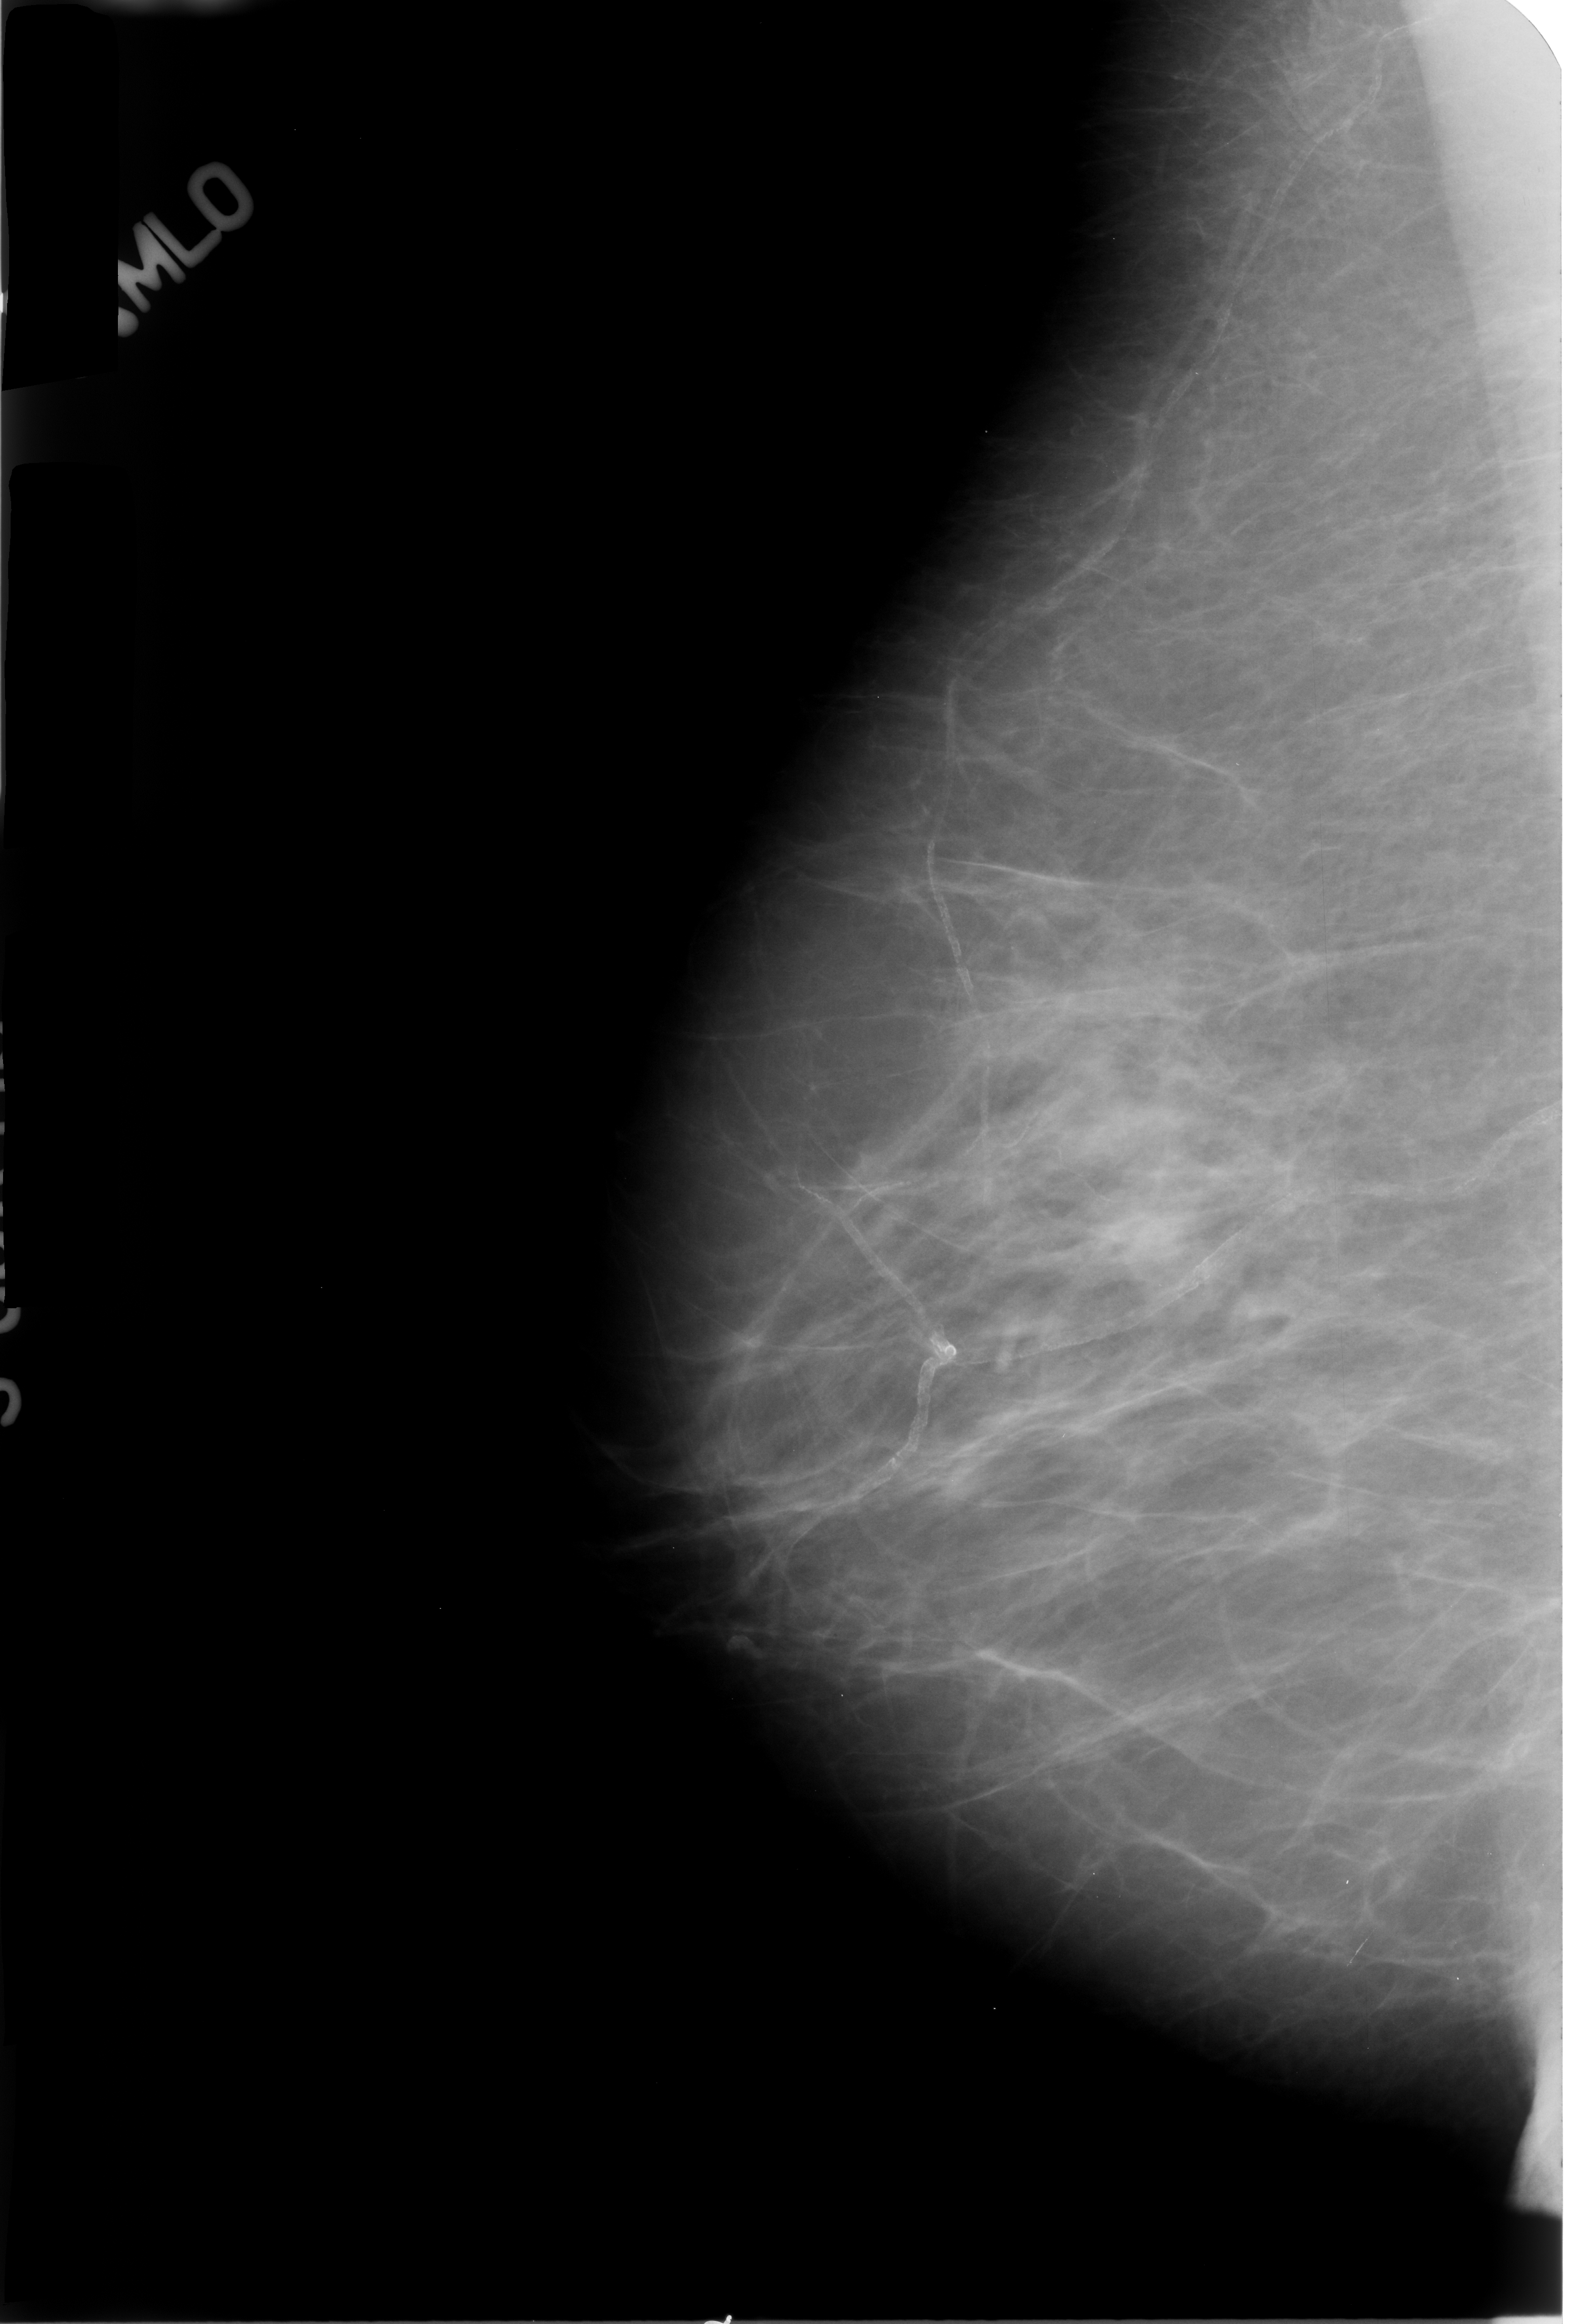
Scanned film-screen mammogram; right breast; mediolateral oblique (MLO) view; breast composition: scattered fibroglandular densities (BI-RADS density category 2 of 4).
Radiologist-marked abnormalities on this image: Finding 1 of 3: calcifications, morphology vascular; BI-RADS assessment category 2; benign without callback (not worked up further). Finding 2 of 3: calcifications, morphology vascular; BI-RADS assessment category 2; benign without callback (not worked up further). Finding 3 of 3: calcifications, morphology vascular; BI-RADS assessment category 2; benign without callback (not worked up further).